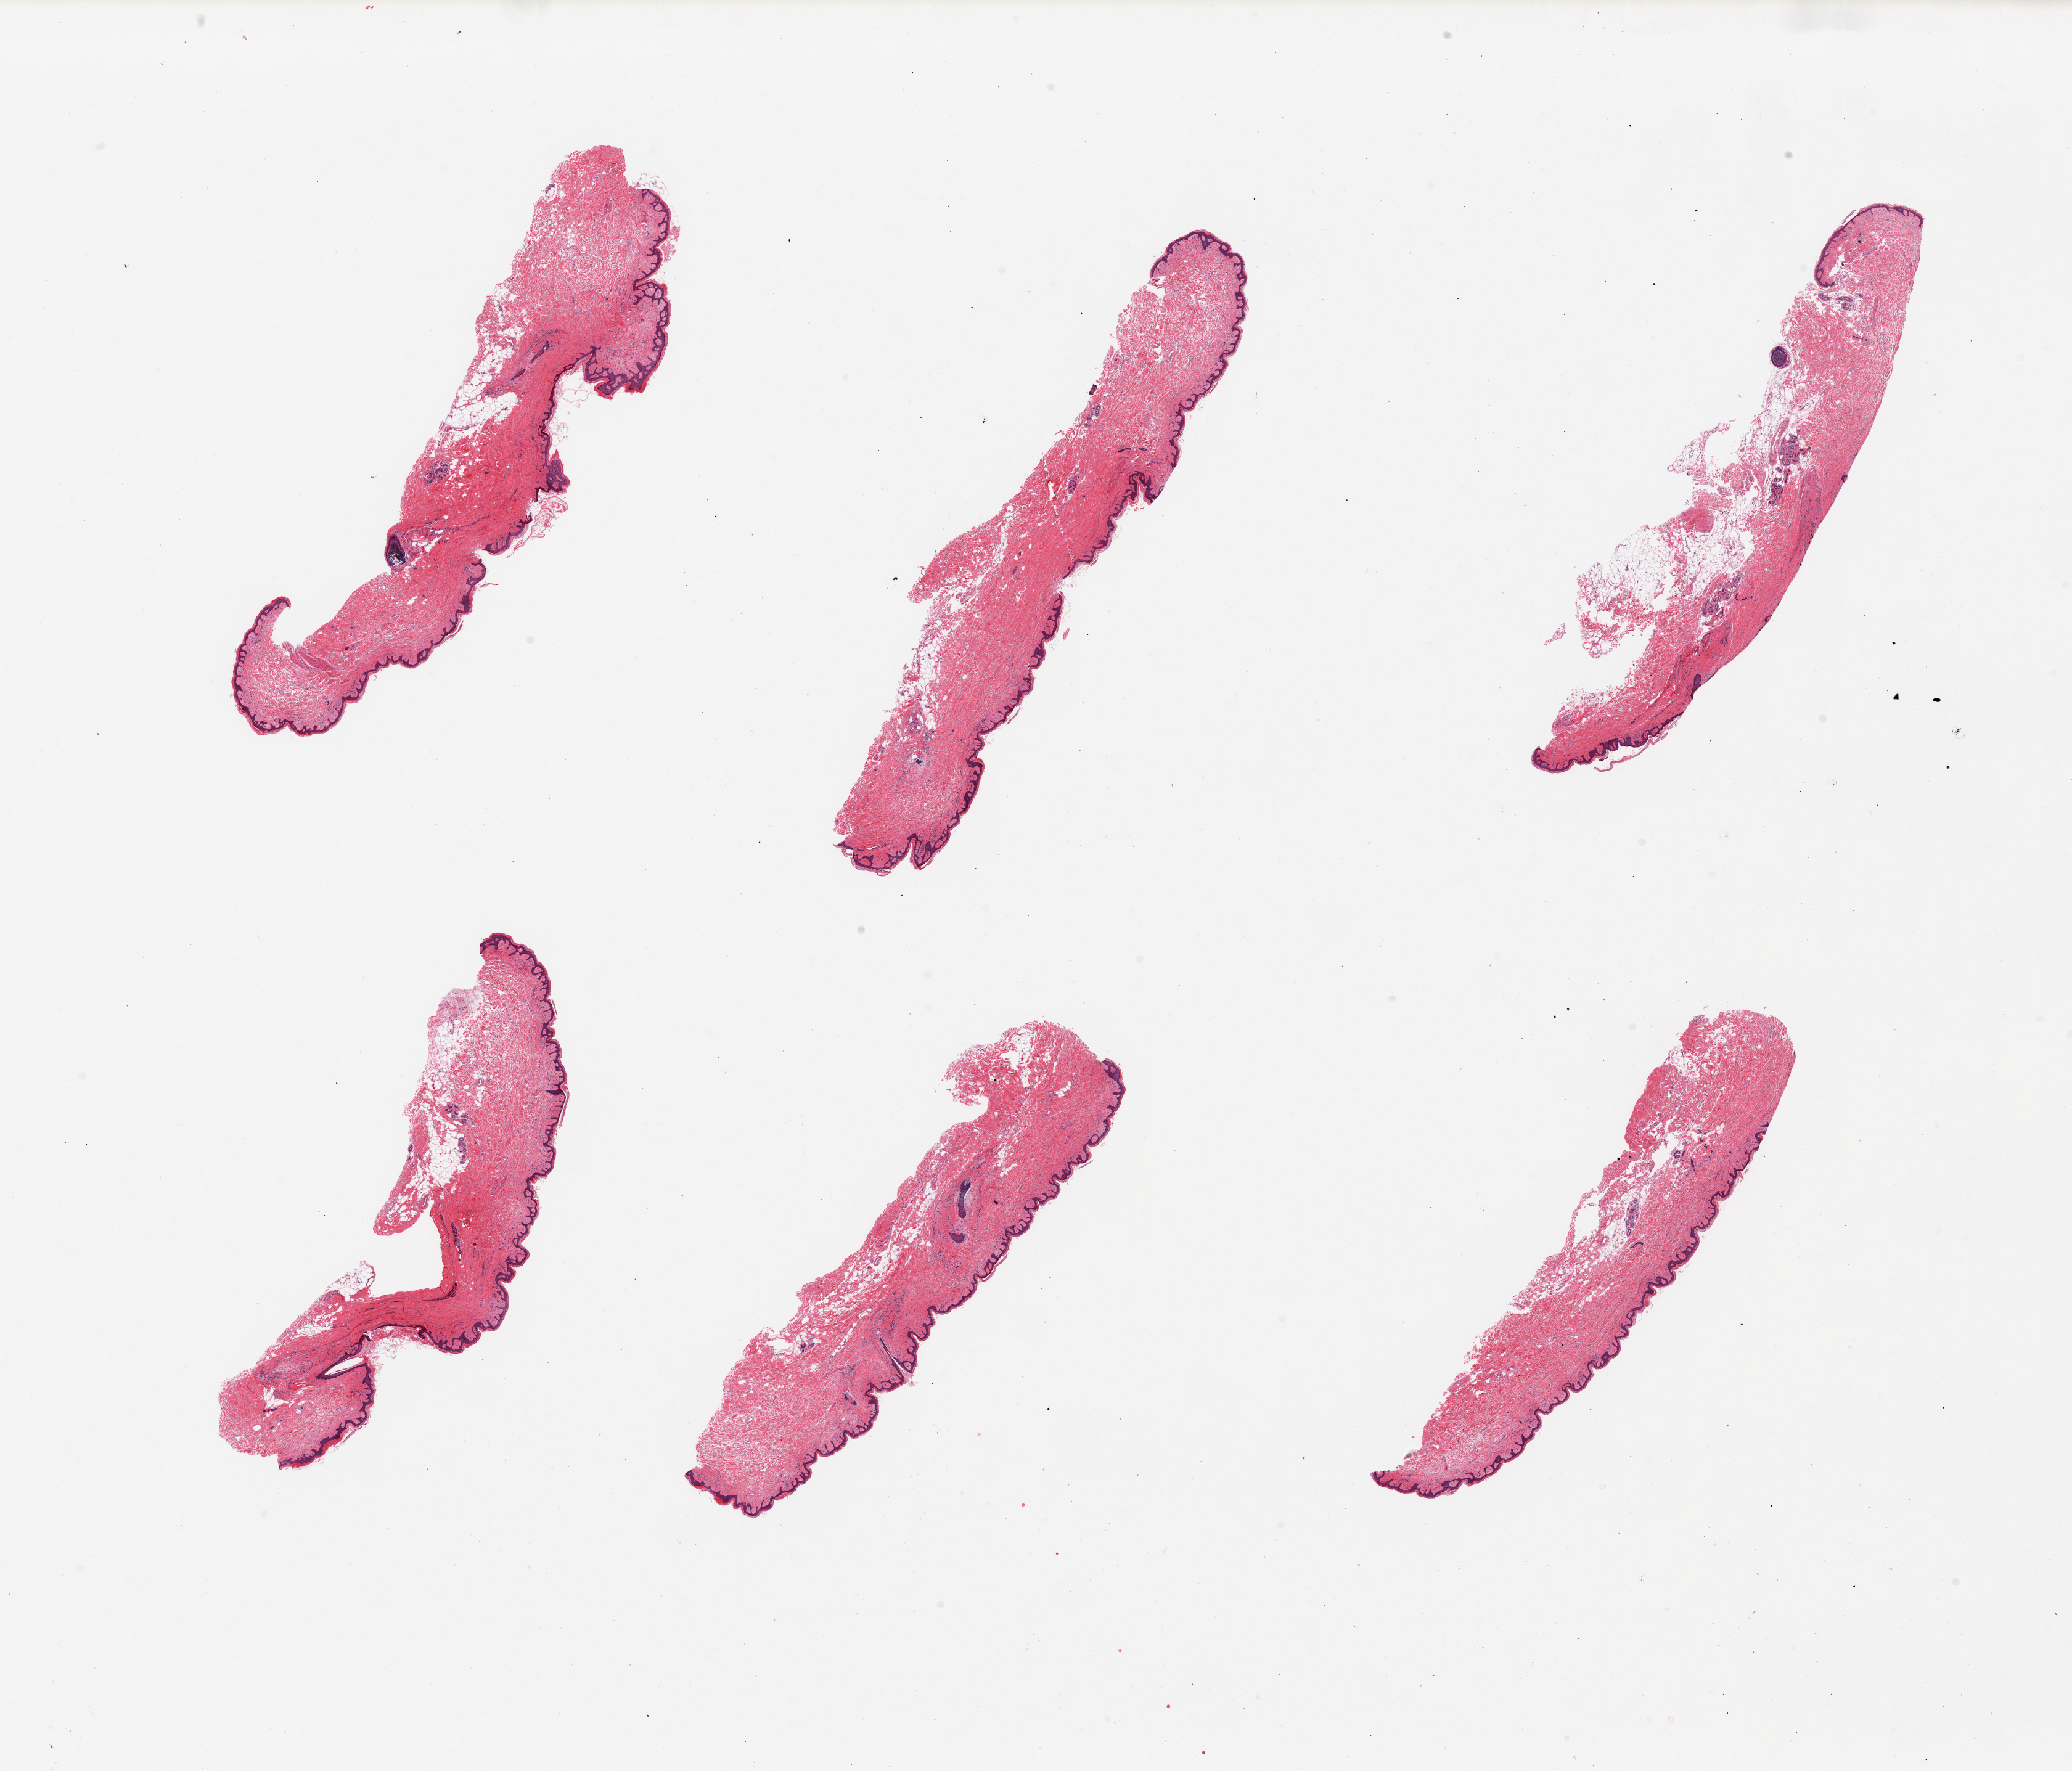
Haematoxylin and eosin whole-slide image, shown as a low-resolution overview of the whole scanned area (about 26.6 x 22.7 mm). PAXgene-fixed paraffin-embedded (PFPE) section. Section of skin of suprapubic region (target tissue). Tissue donor sample. Male donor.
Review note (as recorded): 6 pieces; few sections with residual attached fat up to 20%.